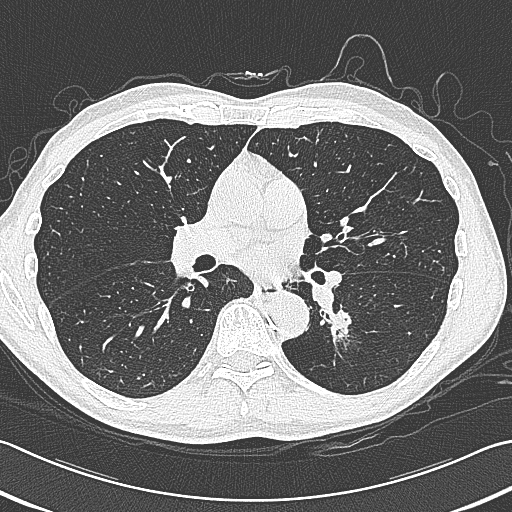
Low-dose screening chest CT, axial slice, first (baseline) screen, lung window (W 1500 / L -600 HU), 1 mm slice thickness, 512 × 512 image matrix, field of view 346 × 346 mm. Male participant, aged 59 years at enrolment. Former smoker at enrolment.
- Expert reader's lesion annotation, bounding box (x1, y1, x2, y2) in pixels: (313, 293, 374, 353).
- Reader record for this screening exam (exam-level; its link to the box is not recorded): non-calcified nodule or mass ≥4 mm, left lower lobe, 15 × 15 mm, smooth margins, soft tissue attenuation.
- Official screen result: positive, change unspecified: nodule(s) >= 4 mm or enlarging nodule(s), mass(es), or other non-specific abnormalities suspicious for lung cancer.
- Later outcome: lung cancer diagnosed 17 days after this screen — squamous cell carcinoma, large cell, nonkeratinizing, NOS, left lower lobe, poorly differentiated (G3), stage IB (AJCC 6th edition), 31 mm at pathology.